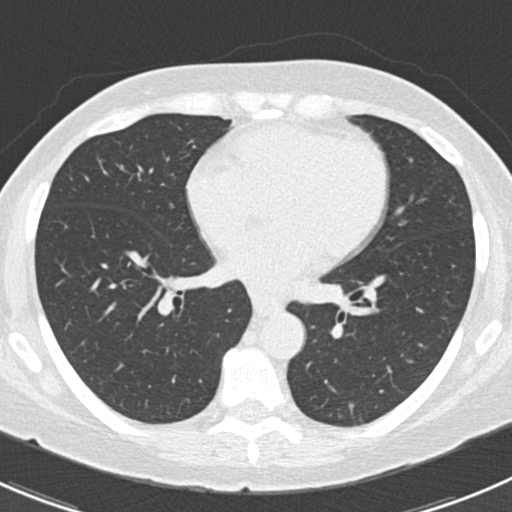
Low-dose screening chest CT, one axial slice. Lung window (W 1500 / L -600 HU). 2 mm slice thickness. 512 × 512 image matrix.
Structures marked on this image (manually delineated by an expert):
- lesion 1 (tumor, lower lobe of left lung): bounding box <349,404,354,412> (left, top, right, bottom; pixels)